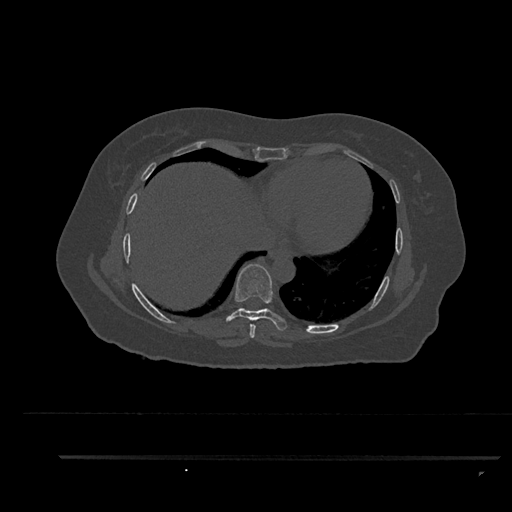
CT including the spine, one axial slice; position 463 of 797 along the scan axis; 120 kVp; bone window (W 1800 / L 400 HU); 512 × 512 image matrix, field of view 408 × 408 mm. Patient: female, 44 years. Case-level facts recorded for this patient, not image findings: primary cancer: renal; vertebrae with lytic lesions (as recorded): L1.
Structures marked on this image (semi-automatically segmented with operator editing):
- T7 vertebra: bounding box (x1, y1, x2, y2) in pixels: (249, 324, 256, 338)
- T8 vertebra: (226, 264, 287, 331)